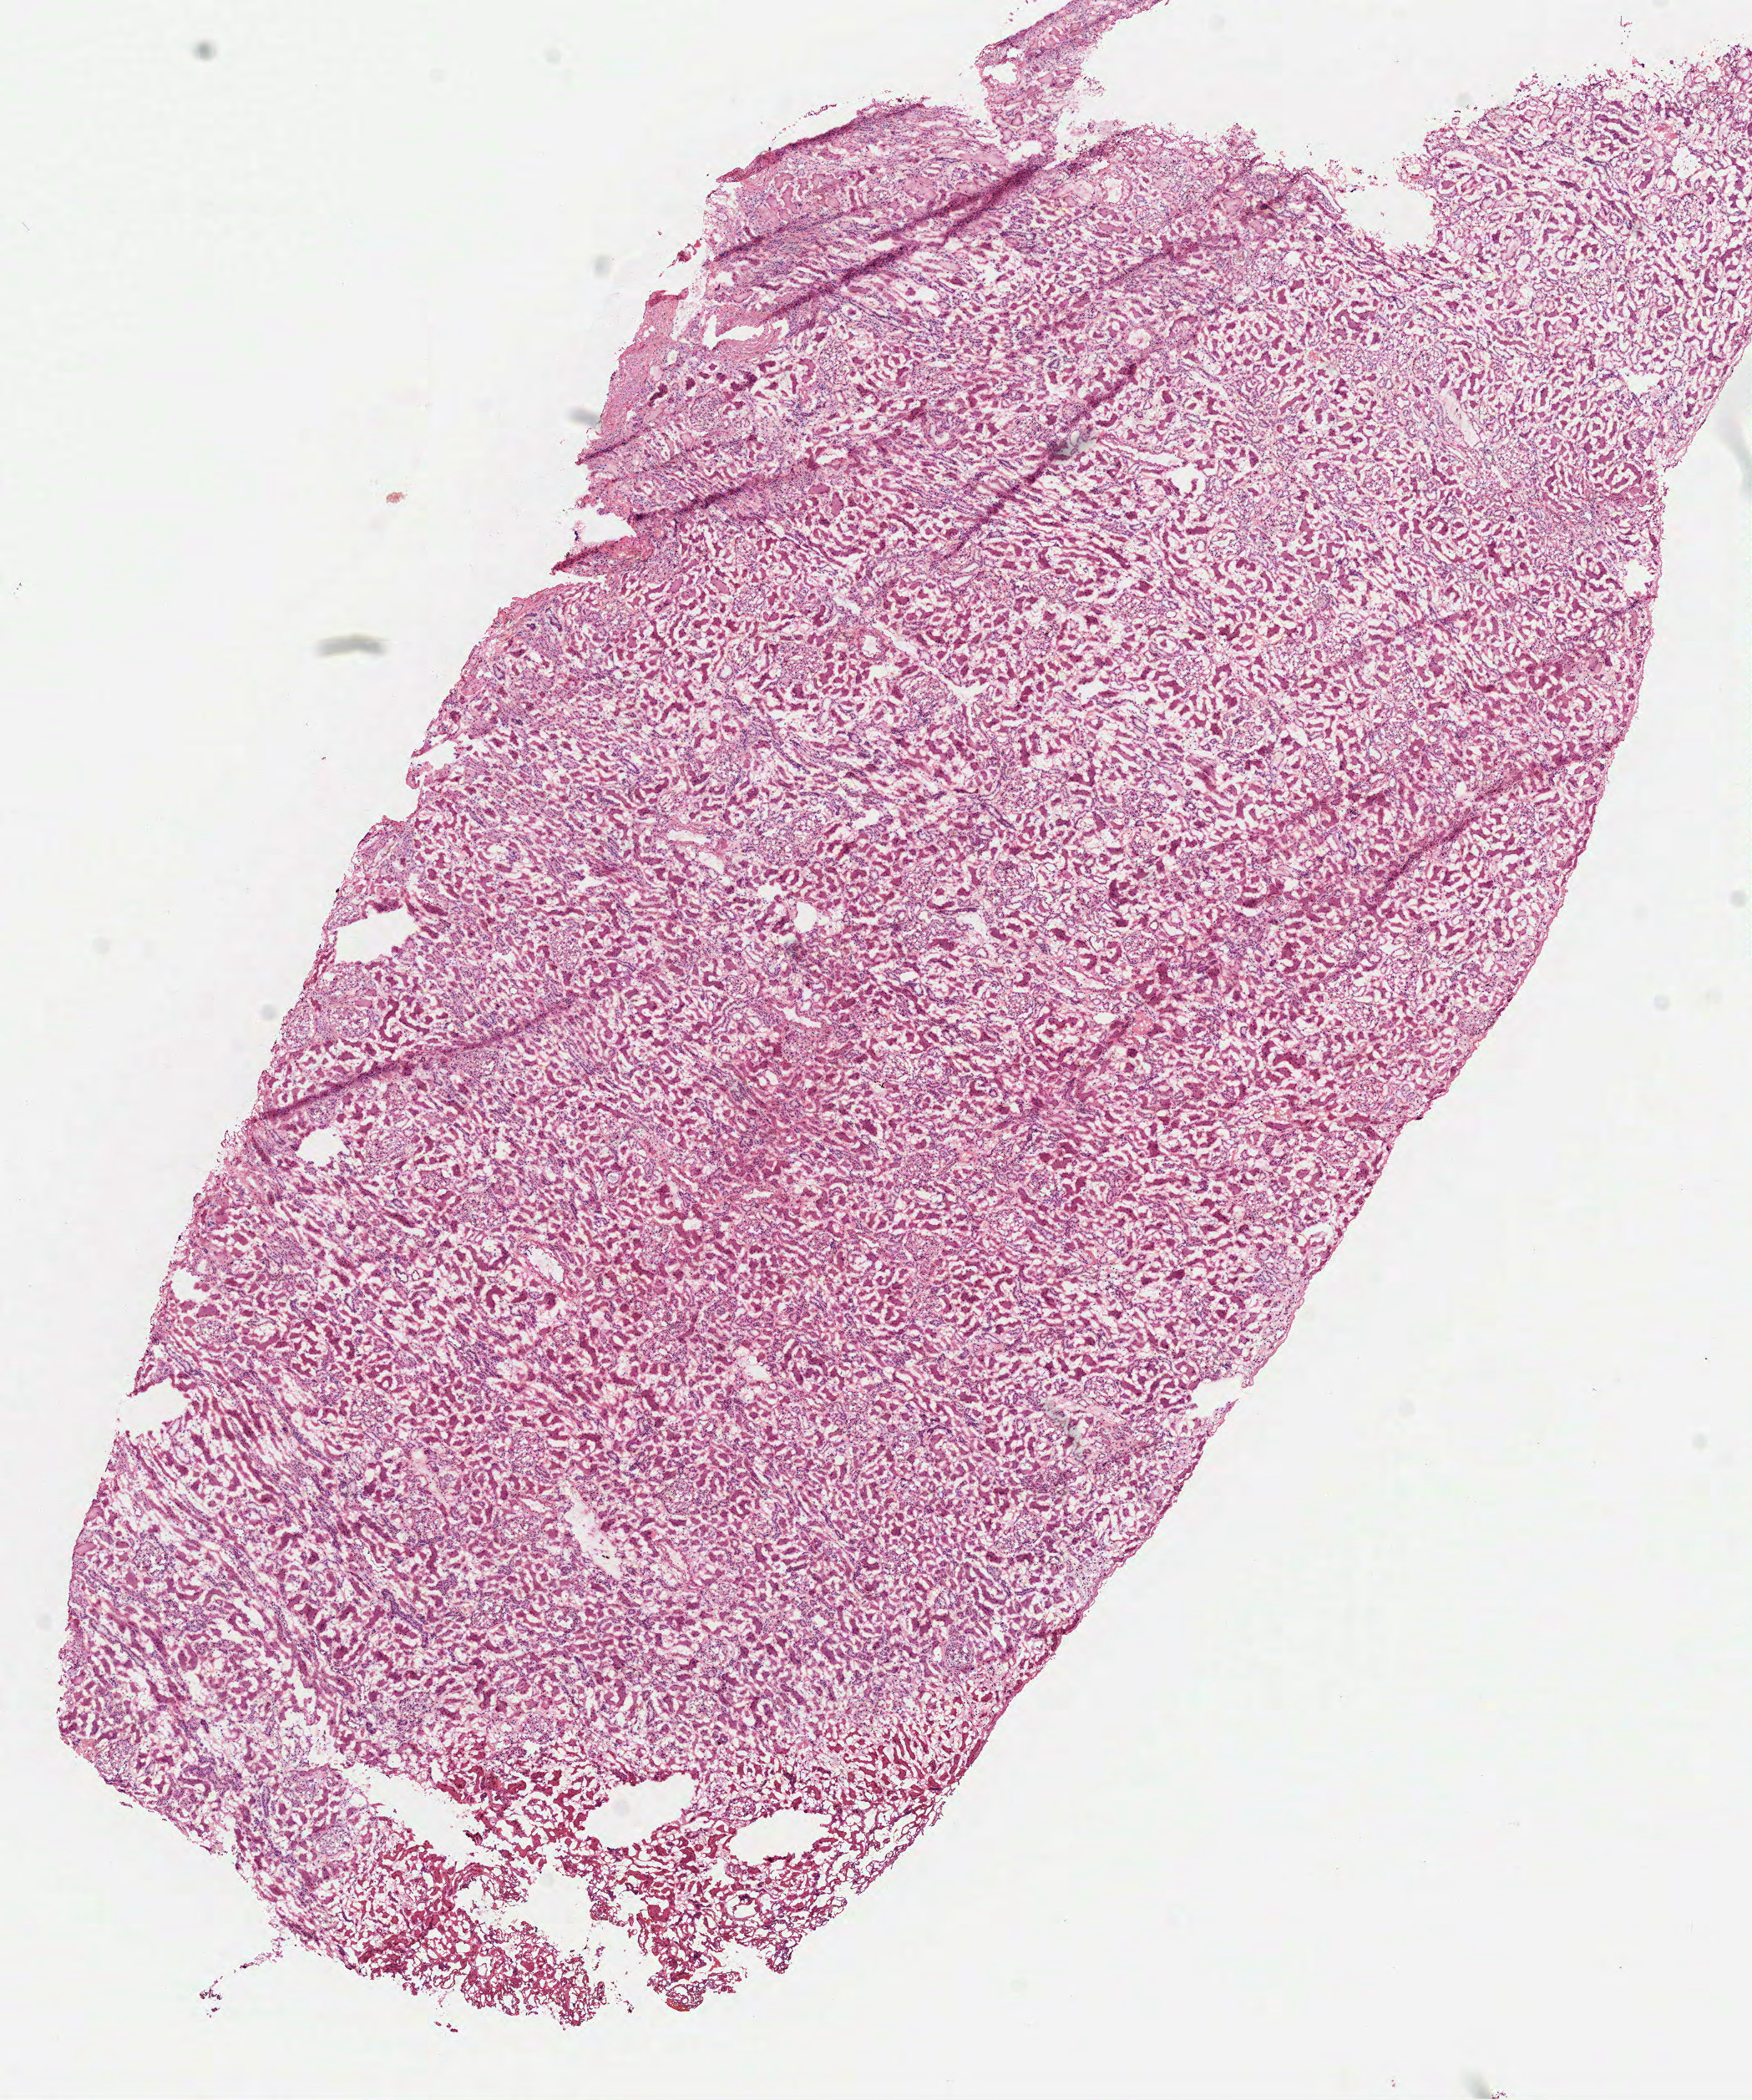
Digitized H&E tissue section (whole slide), shown as a low-resolution overview of the whole scanned area (about 8.5 x 10.1 mm), frozen section from the top of the tissue portion, kidney, solid tissue normal (non-tumour tissue) sample. Patient: male, age at initial diagnosis 61 years.
- this section: solid tissue normal (non-tumour) sample from the same patient
- patient diagnosis: Papillary adenocarcinoma, NOS